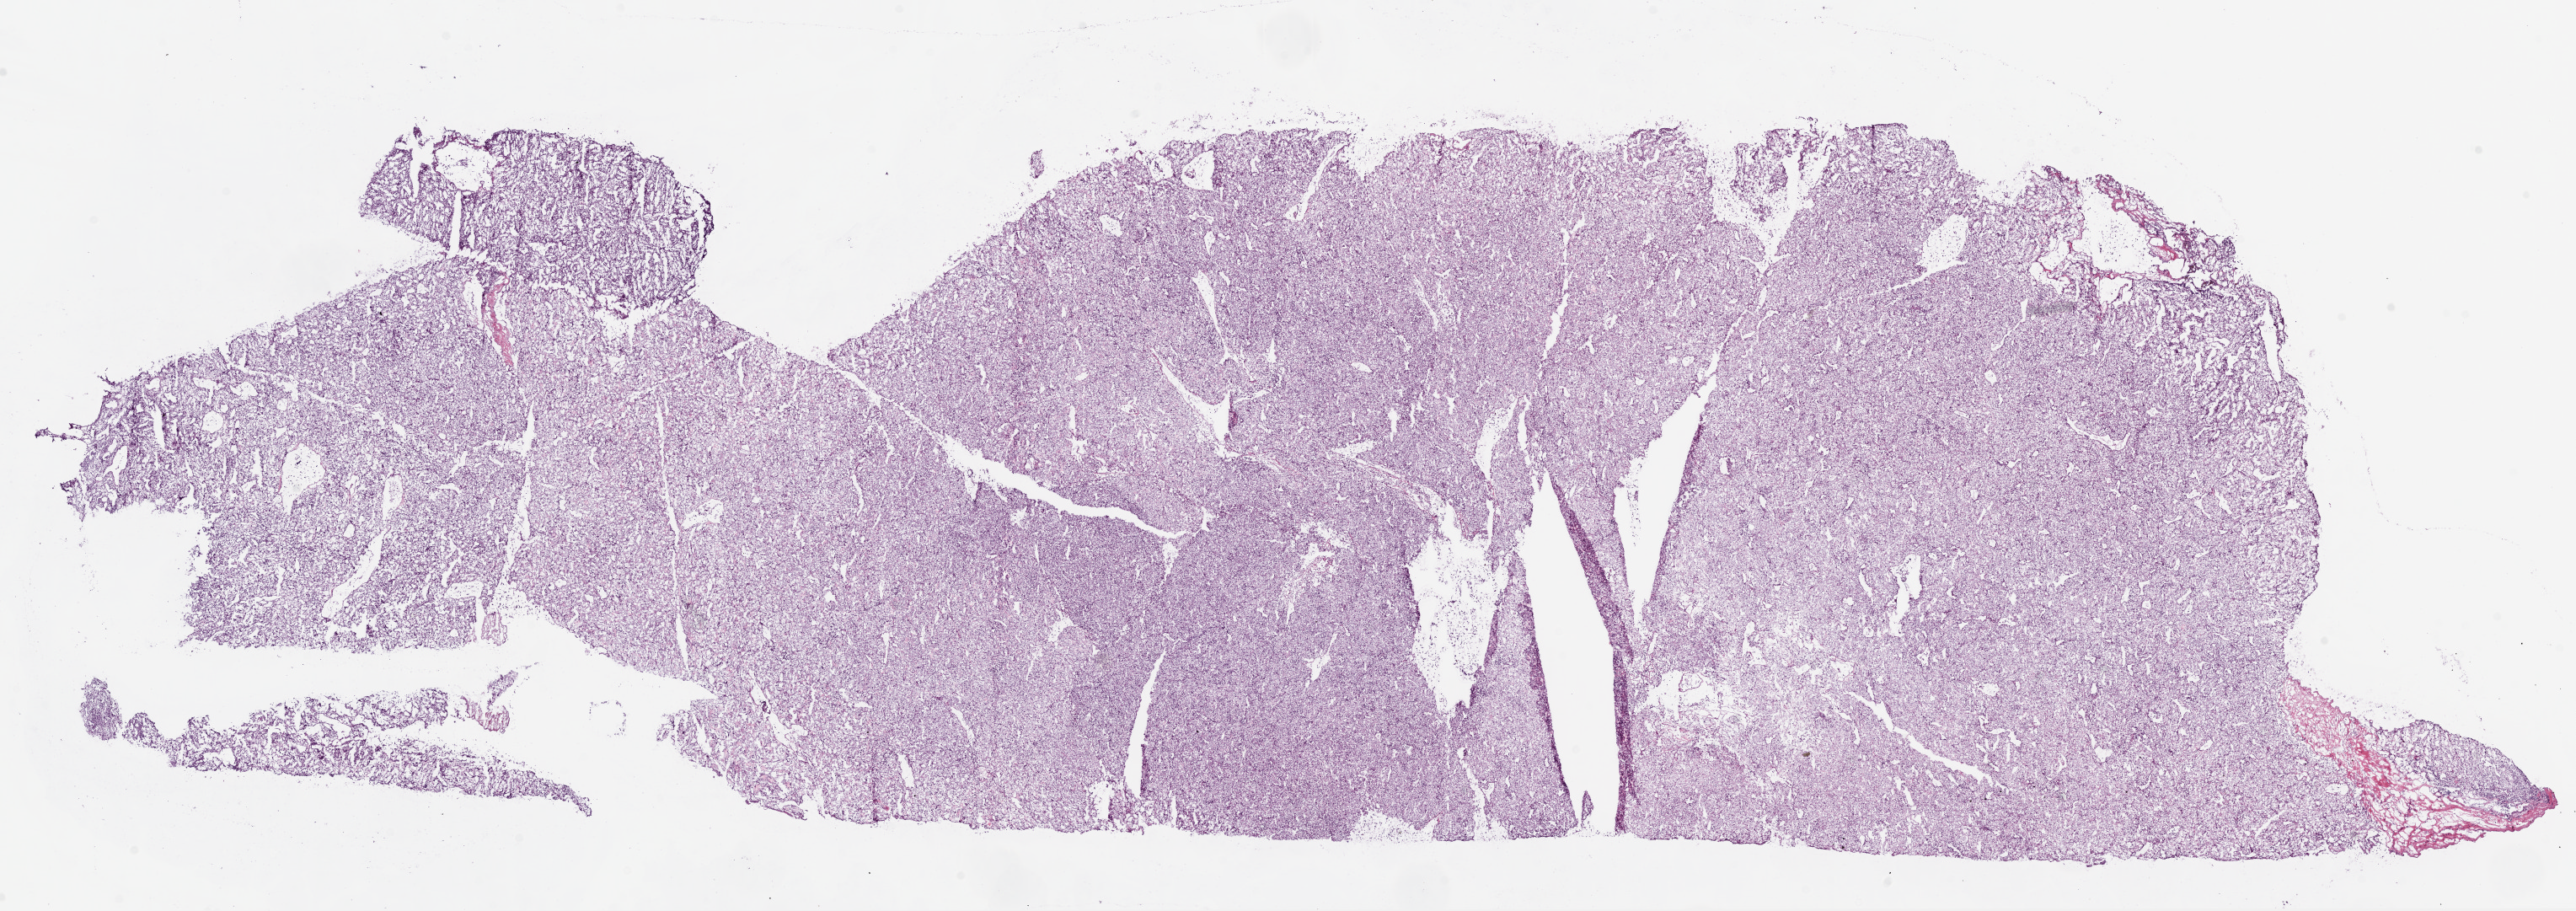
Digitized Hematoxylin and eosin (H&E) stained tissue section (whole slide) — shown as a low-resolution overview of the whole scanned area (about 24.7 x 8.7 mm), frozen section from the top of the tissue portion, sample: primary tumour, kidney. Patient: male, age at initial diagnosis 62 years. Histologic grade: G3 (poorly differentiated). Composition of this section per pathologist review: tumour cells 95%, tumour nuclei 85%, normal cells 0%, stromal cells 5%, necrosis 0%.
AJCC pathologic stage: IV. Lymph nodes positive (case pathology): 0 of 1 examined. Laterality: left. Histologic diagnosis: Clear cell adenocarcinoma, NOS.